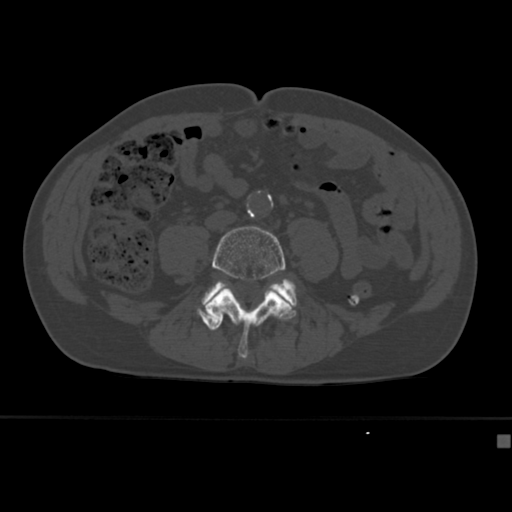
CT including the spine, one axial slice; position 102 of 430 along the scan axis; bone window (W 1800 / L 400 HU); 1.5 mm slice thickness; 512 × 512 image matrix, field of view 337 × 337 mm. Male patient, age 64 years. Case-level facts recorded for this patient, not image findings: primary cancer: uterus.
Outlined on this slice (semi-automatic segmentation, software-assisted and operator-edited):
- L4 vertebra: bounding box [x1, y1, x2, y2] px = [204, 226, 295, 359]
- L5 vertebra: [201, 279, 298, 308]